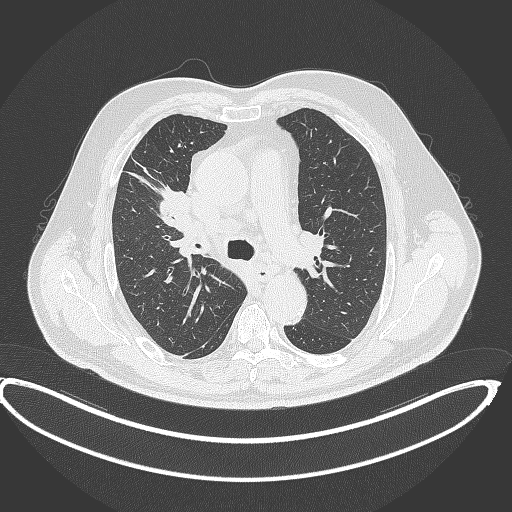
Chest CT, one axial slice; slice 271 of 390 in the series (ordered by position); reconstruction kernel B70f; 120 kVp; lung window (W 1500 / L -600 HU); 1 mm slice thickness; 512 × 512 image matrix. Patient: male, 62 years. Case-level facts recorded for this patient, not image findings: clinical TNM (as recorded): T1c N3 M1c.
Structures marked on this image (bounding box drawn by a radiologist):
- lung tumour (recorded histology: adenocarcinoma): box from (x=160, y=180) to (x=196, y=234) px